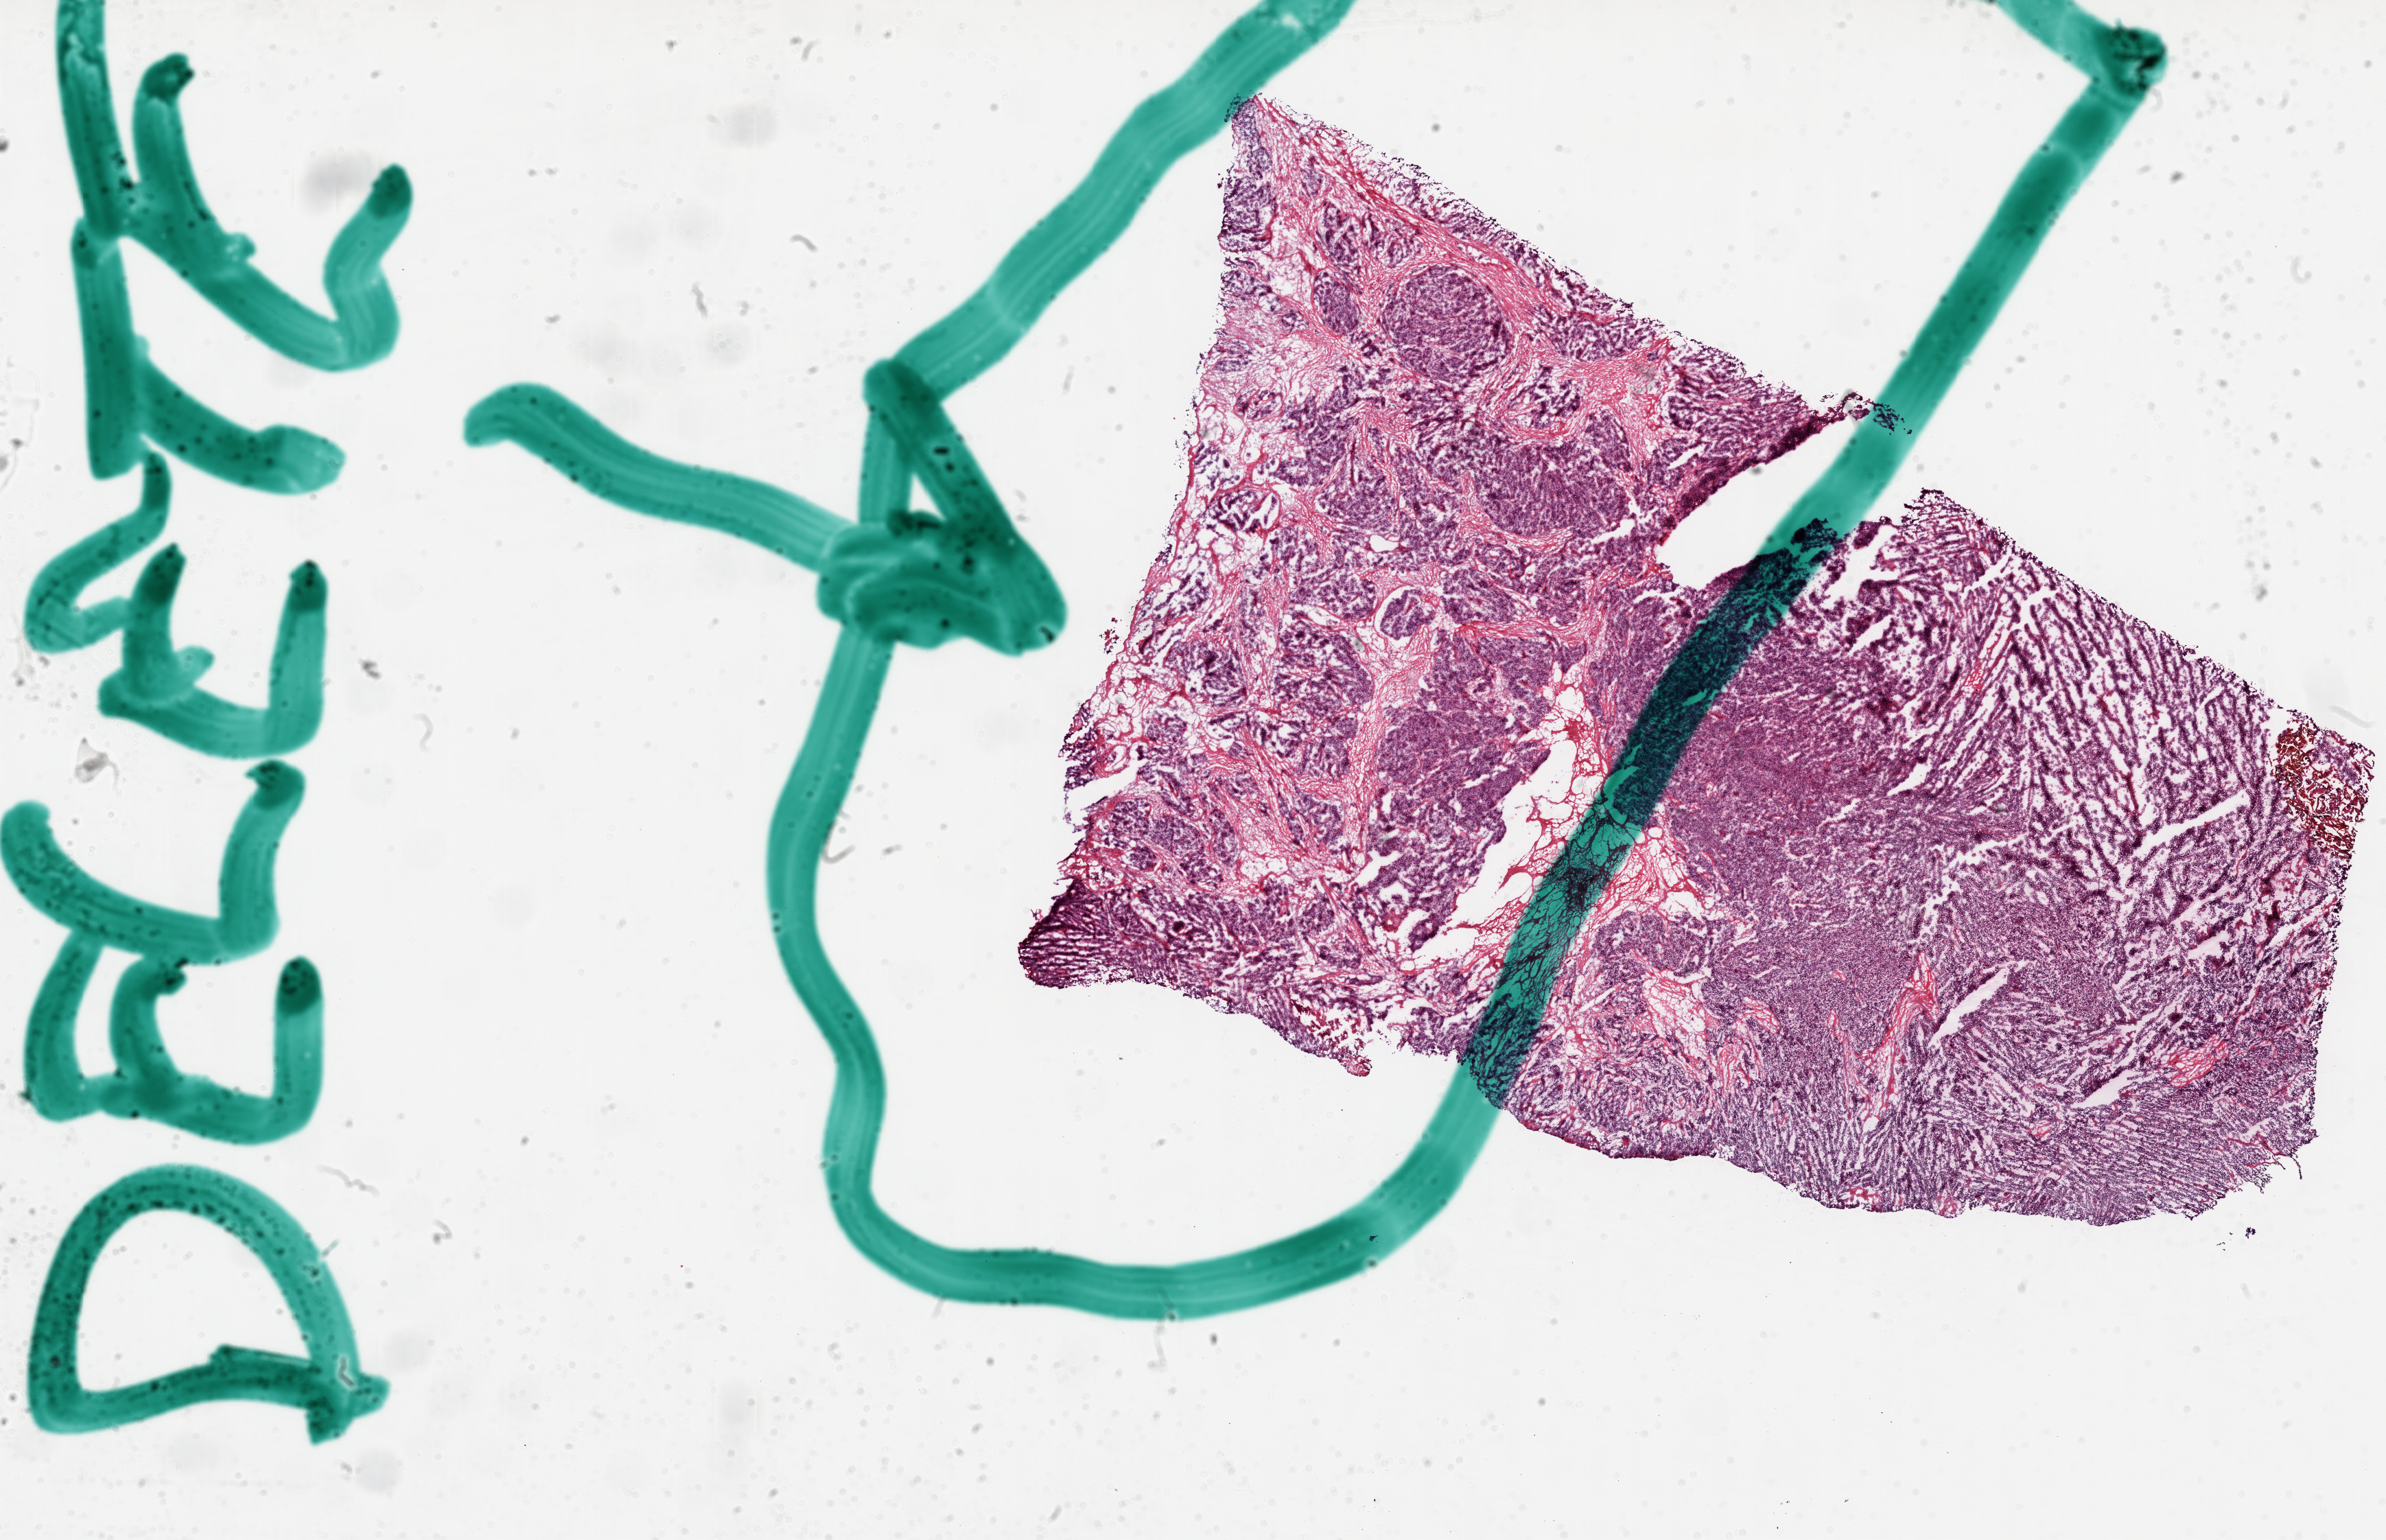
Digitized H&E-stained tissue section (whole slide) — a low-resolution overview of the entire scanned area, about 28.0 x 18.1 mm (acquisition: 20x scan); frozen section; primary tumour sample from the ovary. Female, age 63 years at initial diagnosis. Histologic grade: G3 (poorly differentiated). Pathologist review of this section (percent, as recorded): tumour cells 80%, tumour nuclei 85%, normal cells 0%, stromal cells 20%, necrosis 0%.
* FIGO stage: IV
* laterality: bilateral
* histologic diagnosis: Serous cystadenocarcinoma, NOS